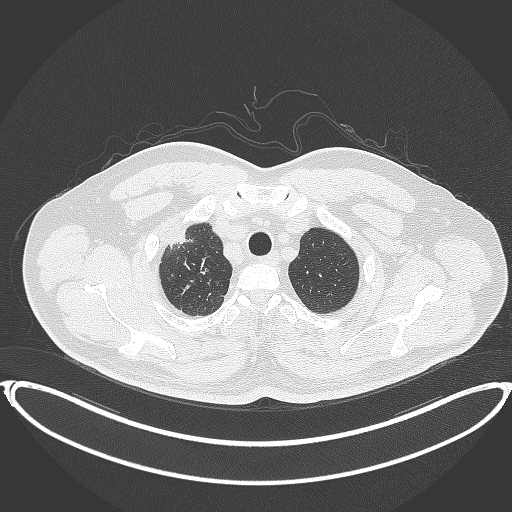
Chest CT, one axial slice. Position 345 of 399 along the scan axis. Reconstruction kernel B70f. 120 kVp. Lung window (W 1500 / L -600 HU). 1 mm slice thickness. 512 × 512 image matrix, field of view 445 × 445 mm. Male patient, age 53 years. Case-level facts recorded for this patient, not image findings: clinical TNM (as recorded): T2a N0 M0.
Structures marked on this image (rectangle marked by the reading radiologist):
- lung tumour (recorded histology: adenocarcinoma): box from (x=163, y=224) to (x=194, y=251) px